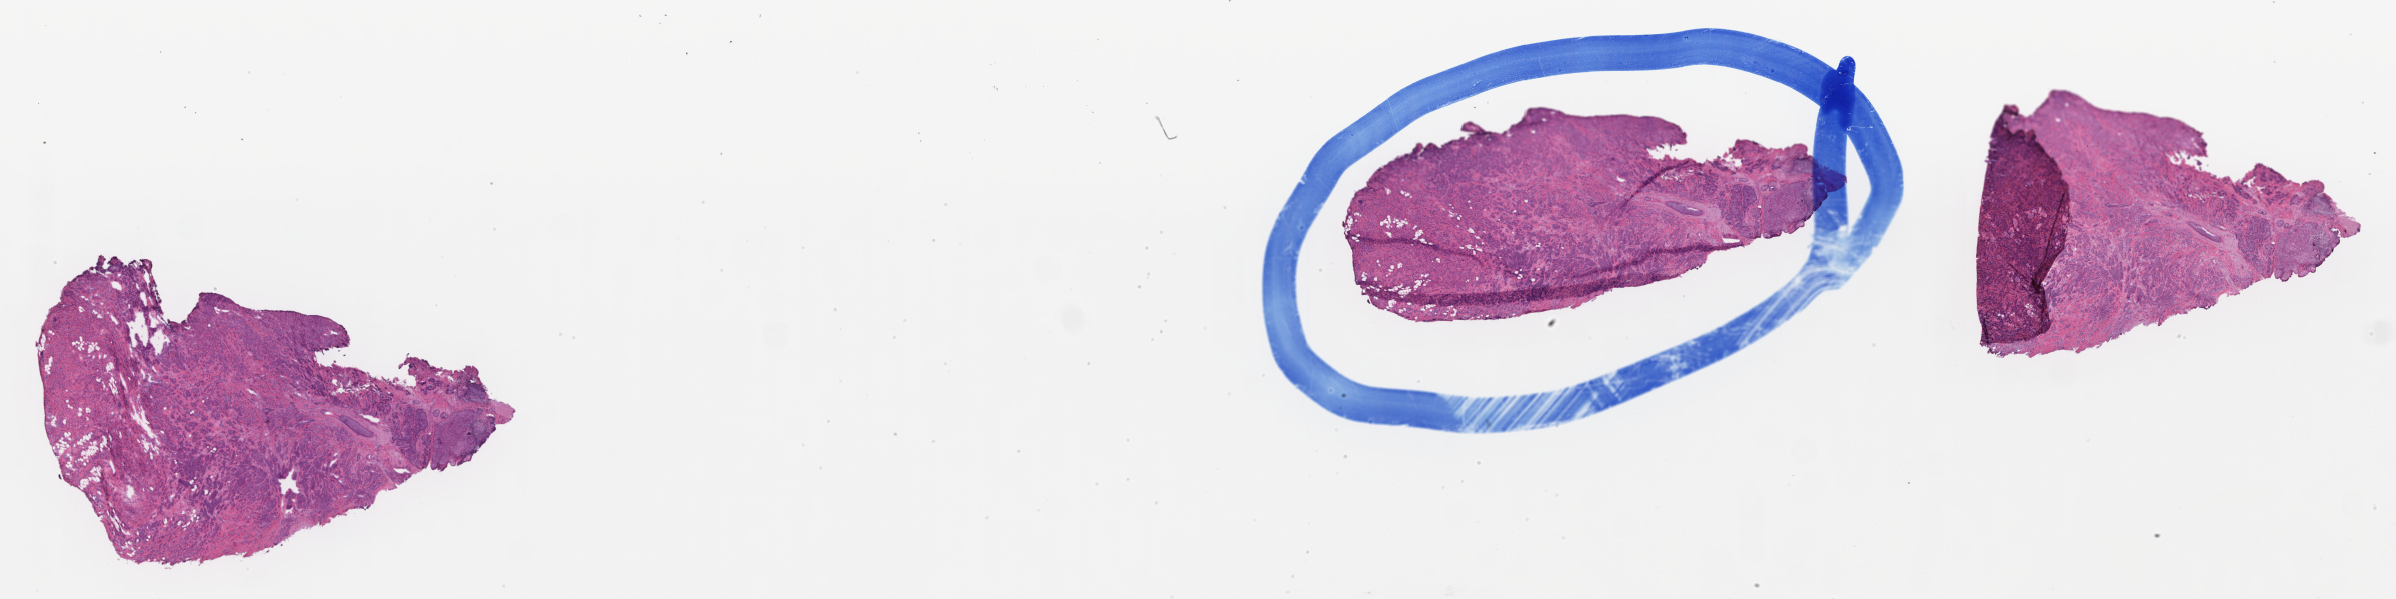
Whole-slide image, haematoxylin and eosin stain, a low-resolution overview of the entire scanned area, about 38.7 x 9.7 mm. Cryosection. Primary tumor. Site: breast (right). Female, age 55 years at initial diagnosis. Slide review estimates, as recorded: tumor cells 65%, tumor nuclei 65%, stromal cells 20%, necrosis 0%, normal cells 15%. Infiltration values recorded for this section: lymphocyte infiltration 10%, monocyte infiltration 2%, neutrophil infiltration 0%.
Section: top of the tissue portion. Histologic diagnosis: Lobular carcinoma, NOS.